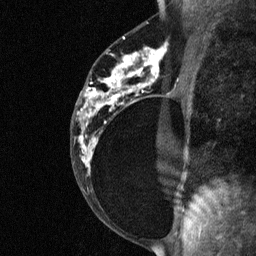
Breast MRI (dynamic contrast-enhanced), one sagittal slice; position 38 of 64 along the scan axis; dynamic contrast-enhanced study with each time point stored as its own series, time point 2 of 3 at this slice position (early post-contrast, ordered by acquisition time); 1.5 T; TE 4.8 ms, TR 27 ms; 256 × 256 image matrix, field of view 180 × 180 mm. Female patient, age 34 years. From the clinical record (not read from this slice): setting: breast cancer imaged before/during neoadjuvant chemotherapy; receptor status: HR-positive, HER2-negative.
Annotated regions visible in this slice (semi-automatically segmented with operator editing):
- analysis volume of interest (the breast-tissue region the enhancement analysis was run in; not a lesion): bounding box [x1, y1, x2, y2] px = [78, 44, 181, 191]
- tumour enhancement mask (voxels above the 90 % enhancement threshold inside the analysis volume of interest): [79, 44, 167, 167]